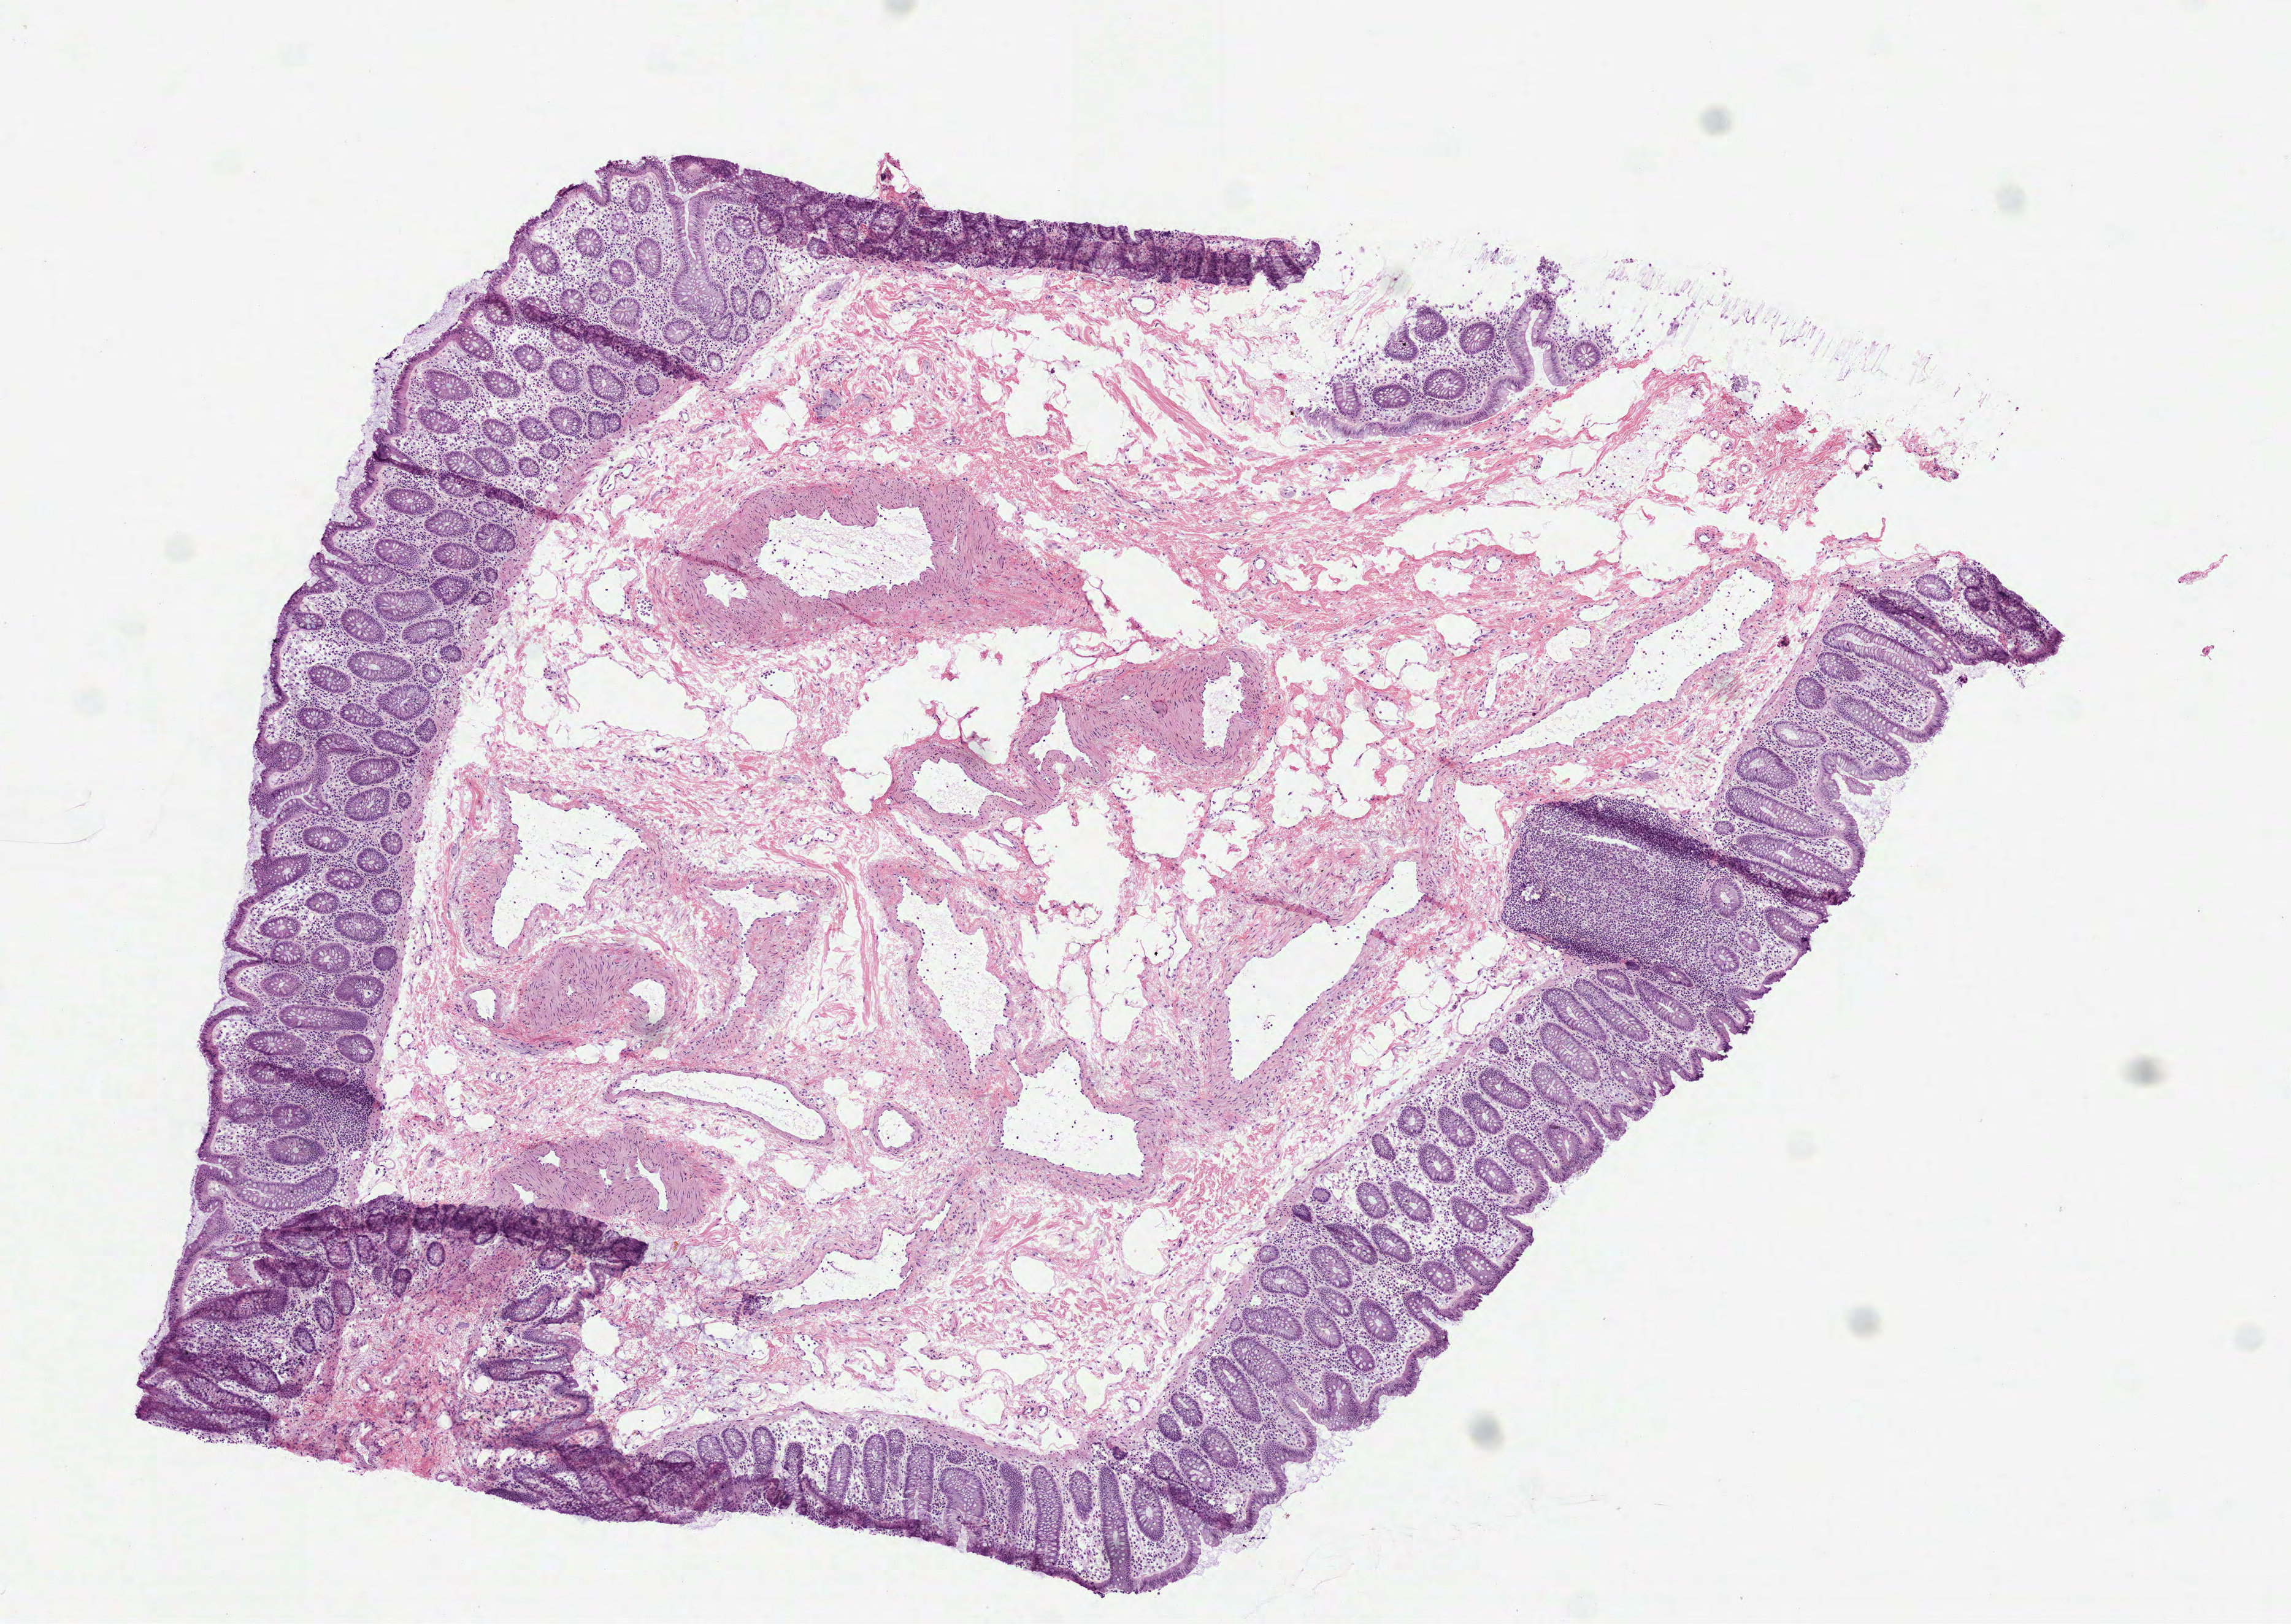
Digitized Hematoxylin and eosin (H&E) stained tissue section (whole slide) — low-resolution overview of the scanned area, about 7.5 x 5.3 mm (from a 40x scan), frozen section from the top of the tissue portion, colon, solid tissue normal (non-tumour tissue) sample. Male patient; age at initial diagnosis 80 years.
• this section: solid tissue normal (non-tumour) sample from the same patient
• patient diagnosis: Adenocarcinoma, NOS (ascending colon)